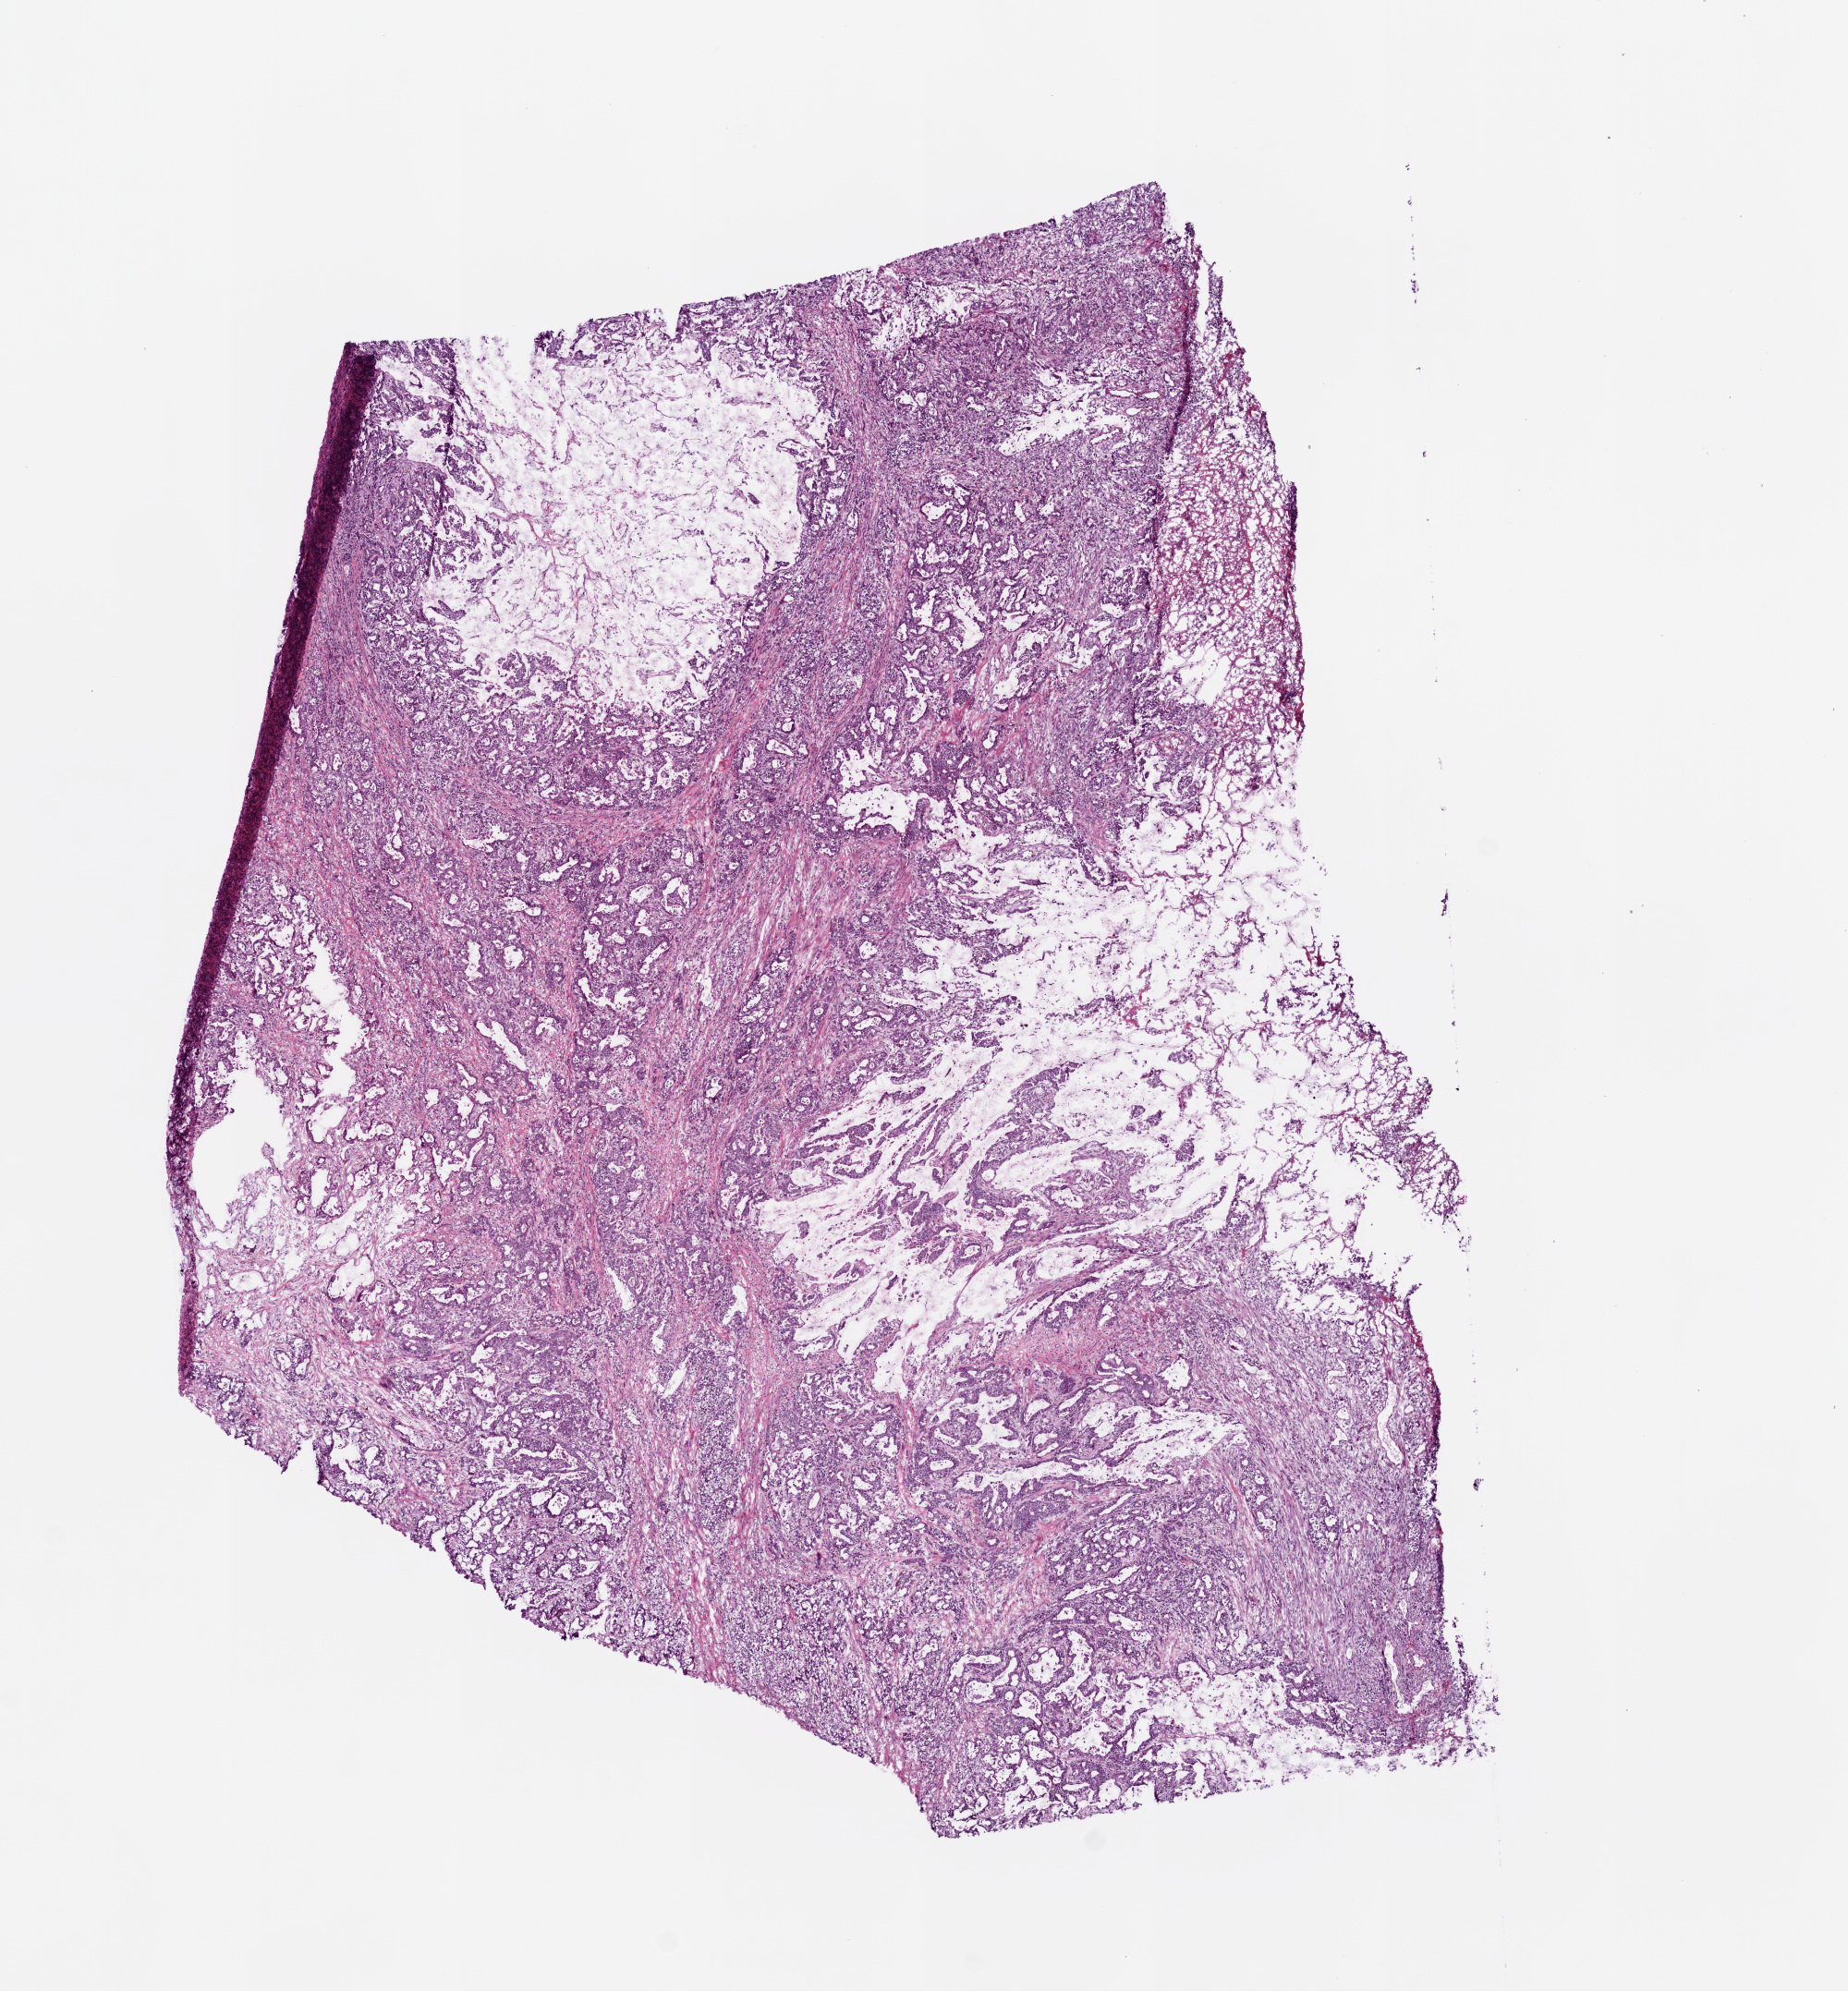
H&E-stained whole-slide image, whole scanned area (about 8.0 x 8.6 mm) shown as a low-resolution overview. Frozen section. Stomach, primary tumour sample. Female, age 83 years at initial diagnosis. Histologic grade: G3 (poorly differentiated). Pathologist review of this section (percent, as recorded): tumour cells 80%, tumour nuclei 80%, normal cells 0%, stromal cells 20%, necrosis 0%.
• lymph nodes positive (case pathology): 7 of 32 examined
• AJCC pathologic stage: IIIA
• diagnosis: Adenocarcinoma, intestinal type (gastric antrum)